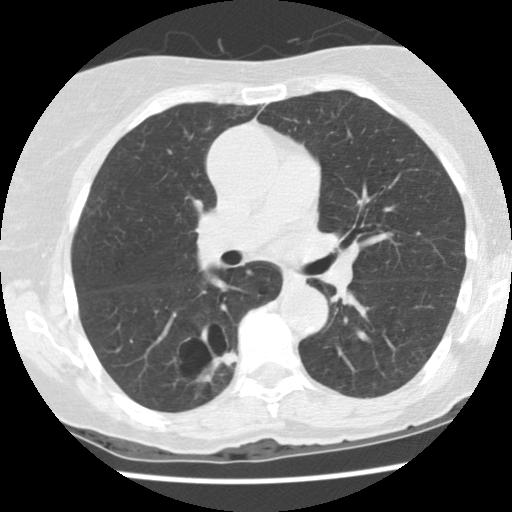
Low-dose screening chest CT, one axial slice. Position 82 of 136 along the scan axis. Reconstruction kernel STANDARD. 120 kVp. Lung window (W 1500 / L -600 HU). 2.5 mm slice thickness. 512 × 512 image matrix.
Structures marked on this image (outlined manually by an expert reader):
- lesion 1 (tumor, lower lobe of right lung): bounding box [x1, y1, x2, y2] px = [198, 352, 236, 381]